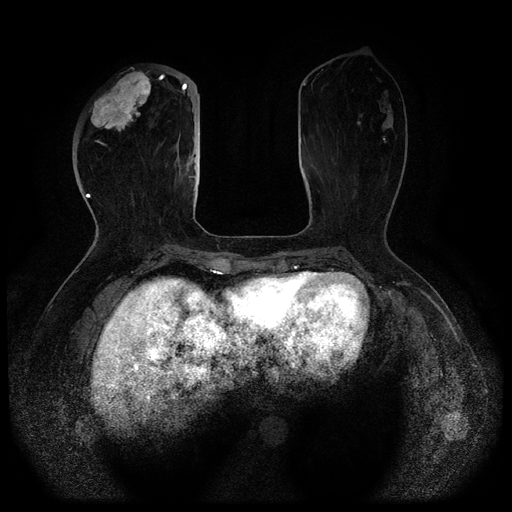
Breast MRI (dynamic contrast-enhanced, multi-phase), one axial slice; dynamic contrast-enhanced series, time point 2 of 5 at this slice position (early post-contrast); 1.5 T; TE 2.6 ms, TR 5.3 ms; 2 mm slice thickness; 512 × 512 image matrix, field of view 350 × 350 mm. Patient: female, 51 years.
Structures marked on this image (semi-automatic segmentation, software-assisted and operator-edited):
- breast lesion (labelled 'tumour' in the annotation; benign lesions carry a separate 'benign' label): bounding box <89,68,151,132> (left, top, right, bottom; pixels)